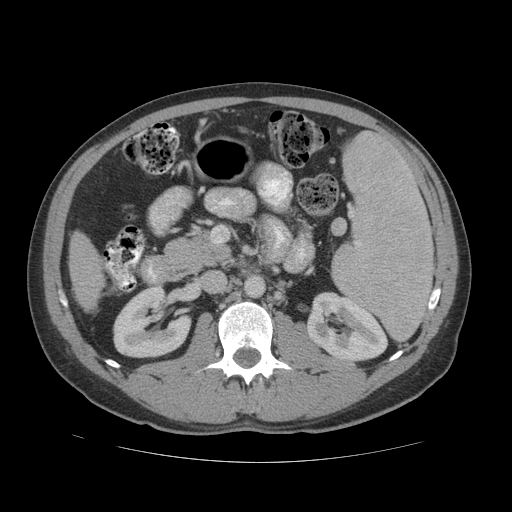
Contrast-enhanced abdominal CT (liver protocol), one axial slice; position 13 of 81 along the scan axis; reconstruction kernel STANDARD; 140 kVp; soft-tissue window (W 400 / L 40 HU); 512 × 512 image matrix, field of view 400 × 400 mm. From the clinical record (not read from this slice): diagnosis: hepatocellular carcinoma (patient treated with transarterial chemoembolisation; whether this scan precedes or follows treatment is not stated here); TNM stage (as recorded): Stage-IVB; Child-Pugh class: B; tumour differentiation: well differentiated.
Structures marked on this image (semi-automatic segmentation, software-assisted and operator-edited):
- liver parenchyma outside the tumour (the mass and vessels are separate outlines, so this box may not span the whole liver): bounding box (x1, y1, x2, y2) in pixels: (68, 232, 104, 308)